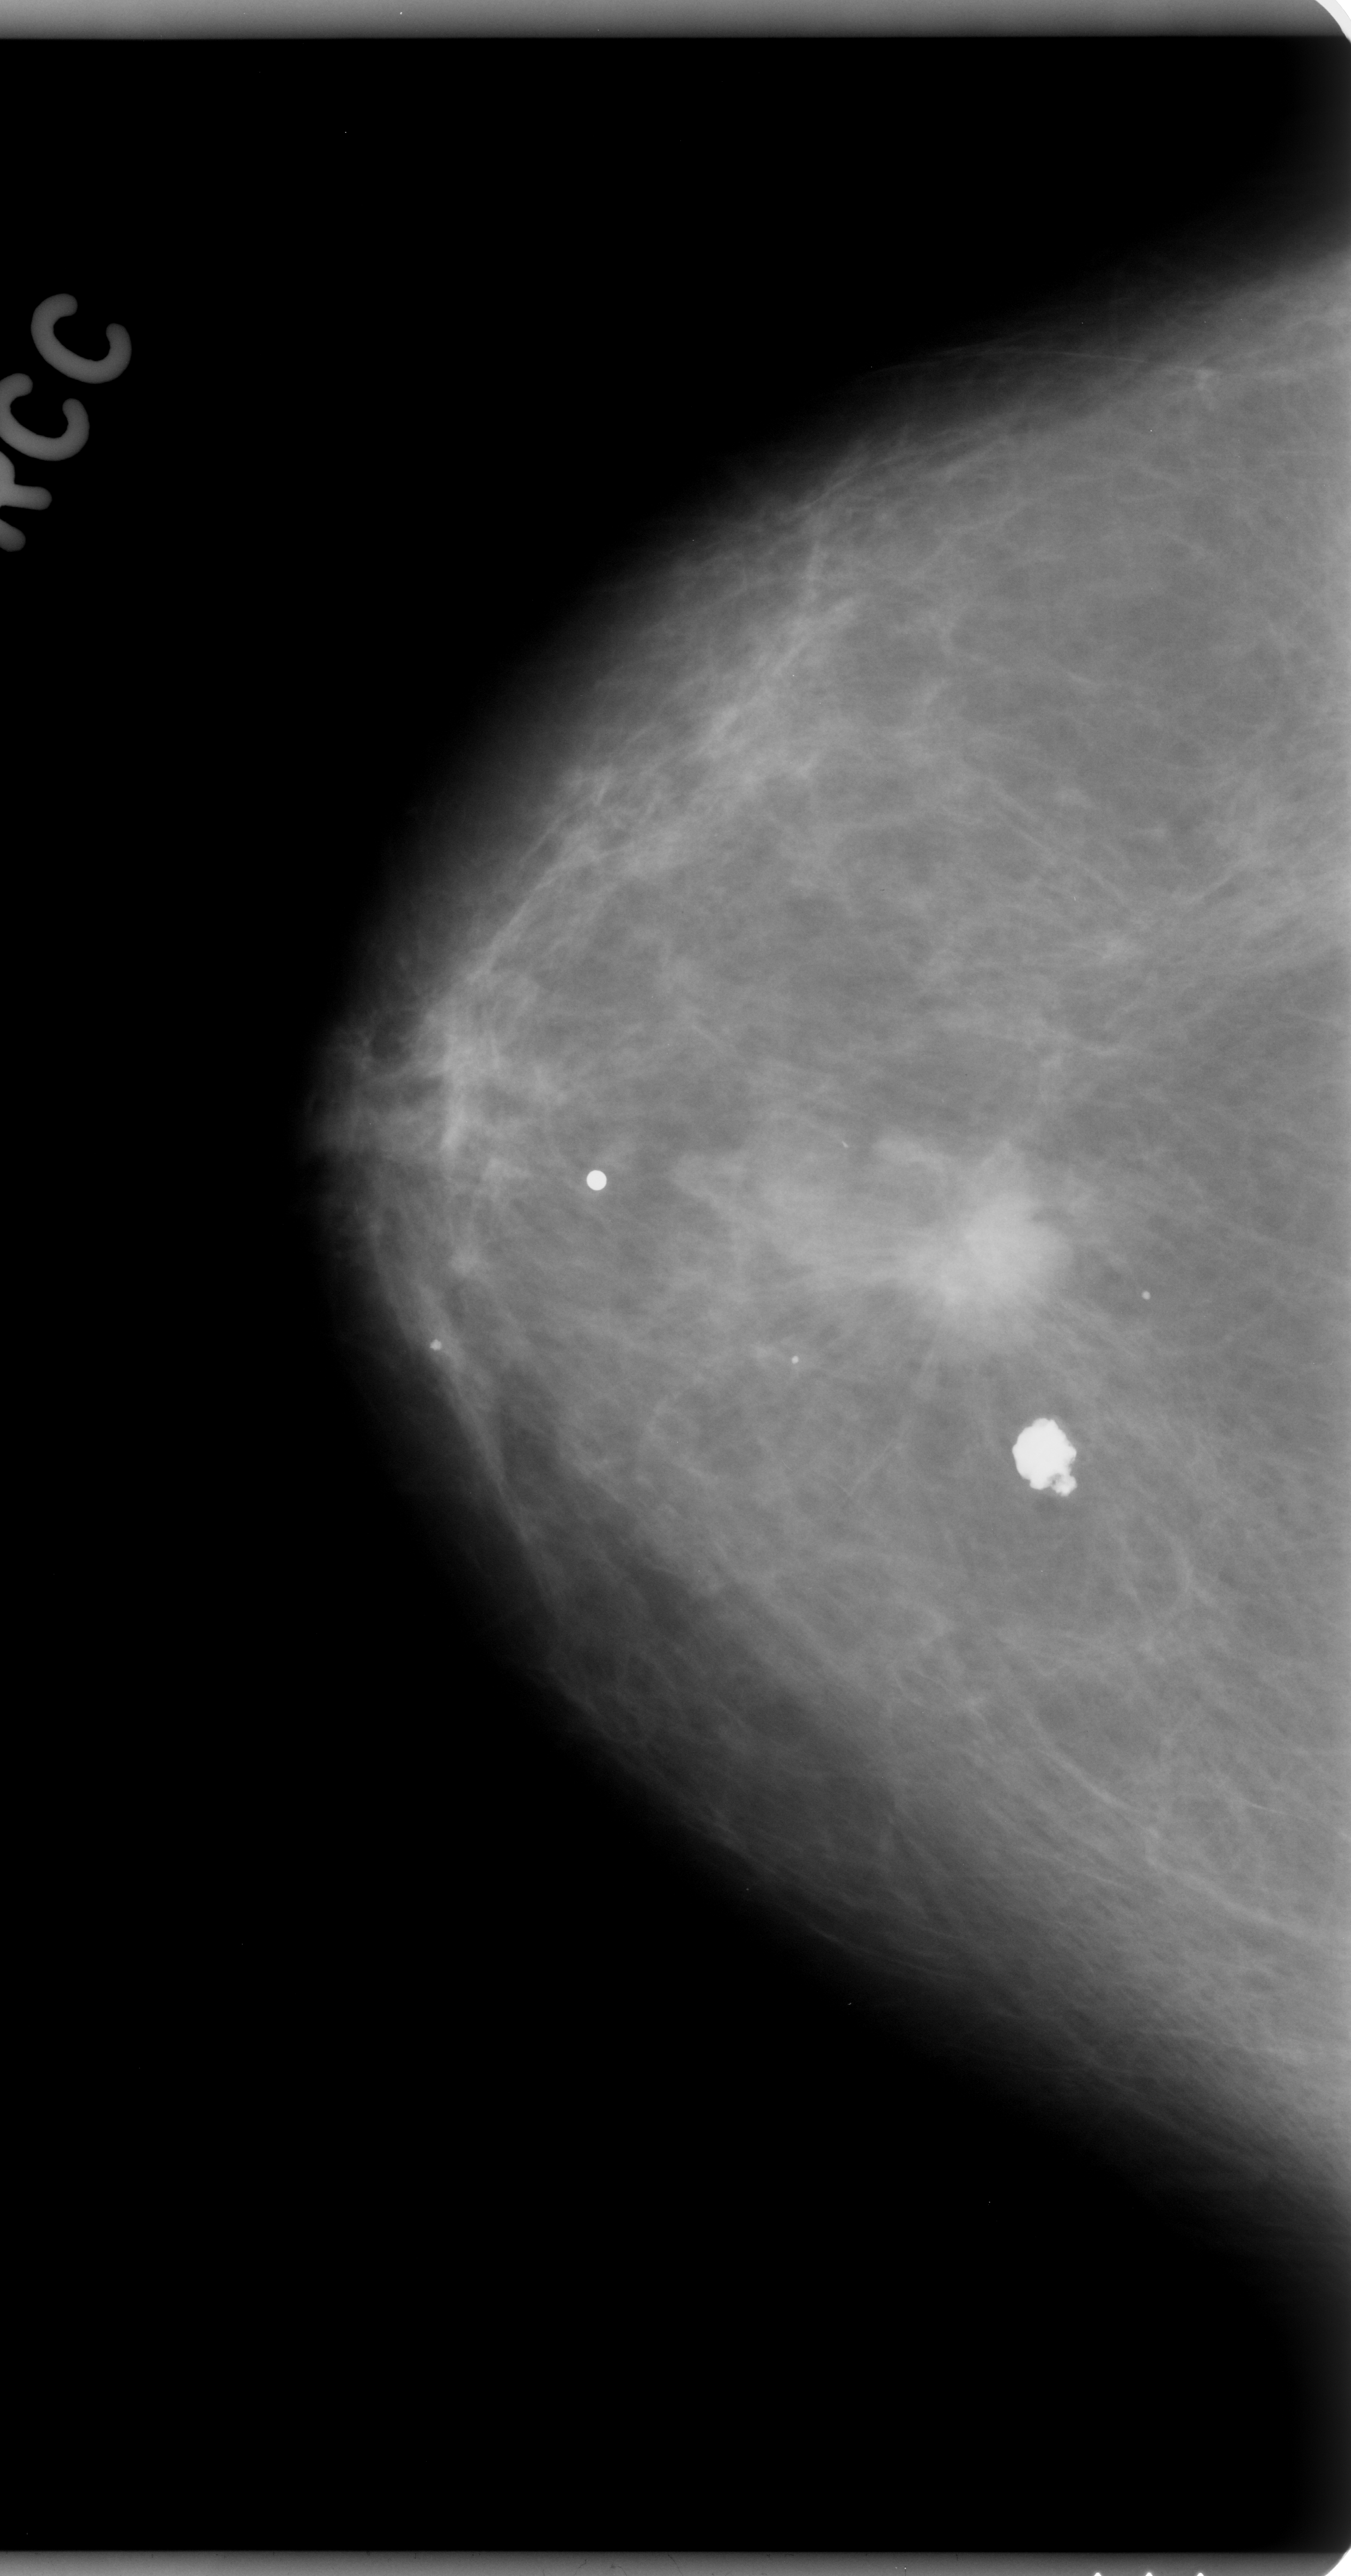
Mammogram (digitized film), right breast, craniocaudal (CC) view, breast composition: almost entirely fatty (BI-RADS density category 1 of 4).
Finding: mass, shape irregular, margins spiculated; BI-RADS assessment category 5; pathology (as recorded): malignant.